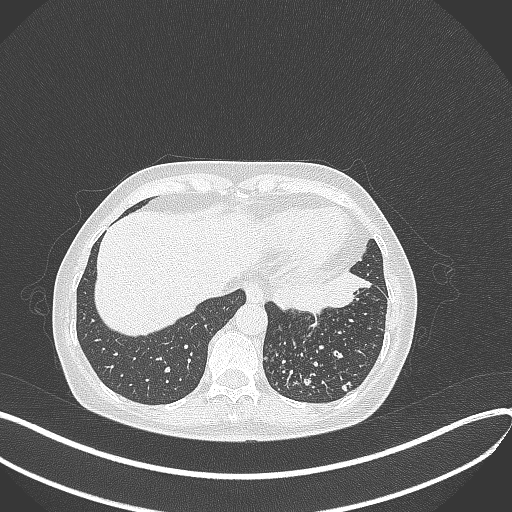
Chest CT, one axial slice. Slice 92 of 429 in the series (ordered by position). 100 kVp. Lung window (W 1500 / L -600 HU). 512 × 512 image matrix, field of view 400 × 400 mm. Female patient, age 63 years. Case-level facts recorded for this patient, not image findings: clinical TNM (as recorded): T1b N0 M0.
Structures marked on this image (rectangle marked by the reading radiologist):
- lung tumour (recorded histology: adenocarcinoma): bounding box [x1, y1, x2, y2] px = [271, 271, 371, 312]